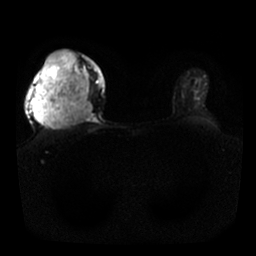
Breast MRI, one axial slice; position 19 of 25 along the scan axis; diffusion-weighted series; image 2 of 4 stored at this slice position (different b-values; order by instance number); 1.5 T; 4 mm slice thickness; 256 × 256 image matrix, field of view 340 × 340 mm. Female patient.
Annotated regions visible in this slice (outlined manually by an expert reader):
- tumour on diffusion-weighted imaging: bounding box <33,51,91,128> (left, top, right, bottom; pixels)